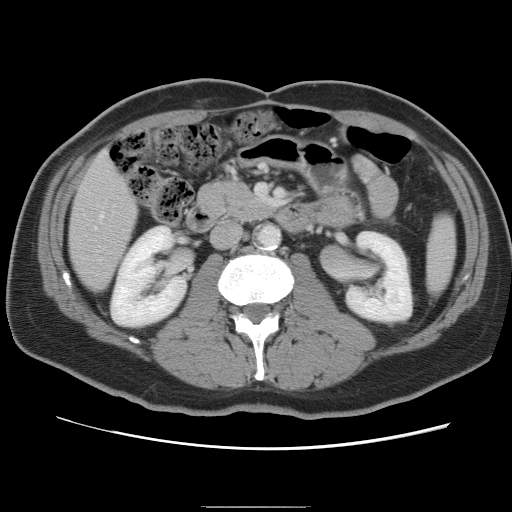
Contrast-enhanced abdominal CT, one axial slice; position 28 of 87 along the scan axis; 120 kVp; intravenous contrast given; soft-tissue window (W 400 / L 40 HU); 5 mm slice thickness; 512 × 512 image matrix. Male patient, age 63 years. From the clinical record (not read from this slice): diagnosis: colorectal cancer liver metastases, imaged before liver resection; multiple liver metastases: no; largest metastasis: 9 cm; disease in both lobes: no.
Structures marked on this image (expert manual segmentation):
- hepatic veins: bounding box [x1, y1, x2, y2] px = [100, 214, 102, 217]
- liver: [70, 153, 138, 290]
- planned liver remnant (the part of the liver to remain after resection): [70, 153, 138, 290]